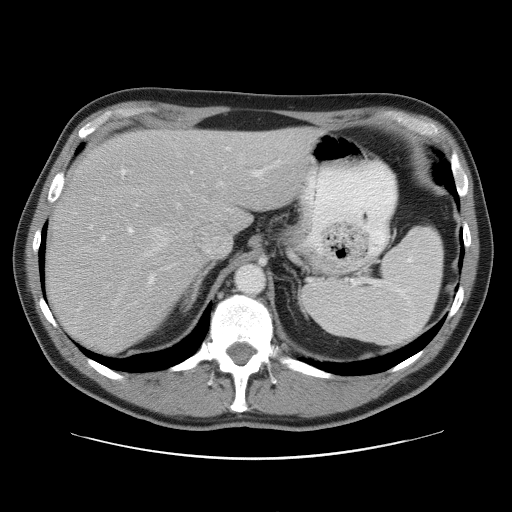
Contrast-enhanced abdominal CT, one axial slice. Slice 41 of 52 in the series (ordered by position). Reconstruction kernel STANDARD. 120 kVp. Intravenous contrast given. Soft-tissue window (W 400 / L 40 HU). 5 mm slice thickness. 512 × 512 image matrix. Male patient, age 70 years. From the clinical record (not read from this slice): diagnosis: colorectal cancer liver metastases, imaged before liver resection; multiple liver metastases: yes; largest metastasis: 4 cm; disease in both lobes: yes.
Outlined on this slice (manually delineated by an expert):
- hepatic veins: box from (x=144, y=155) to (x=243, y=289) px
- liver: (x=46, y=129)–(x=317, y=353)
- planned liver remnant (the part of the liver to remain after resection): (x=109, y=129)–(x=317, y=218)
- portal vein (with intrahepatic branches): (x=121, y=147)–(x=267, y=233)